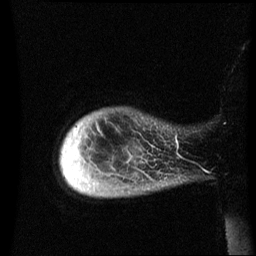
Breast MRI (dynamic contrast-enhanced), one sagittal slice. Dynamic contrast-enhanced series, image 2 of 3 at this slice position (ordered by acquisition). 1.5 T. TE 4.2 ms, TR 8.4 ms. 256 × 256 image matrix, field of view 220 × 220 mm. Female patient, age 49 years.
Annotated regions visible in this slice (semi-automatic segmentation, software-assisted and operator-edited):
- analysis volume of interest (the breast-tissue region the enhancement analysis was run in; not a lesion): box from (x=61, y=108) to (x=185, y=197) px
- tumour enhancement mask (voxels above the 70 % enhancement threshold inside the analysis volume of interest): (x=98, y=126)–(x=179, y=149)